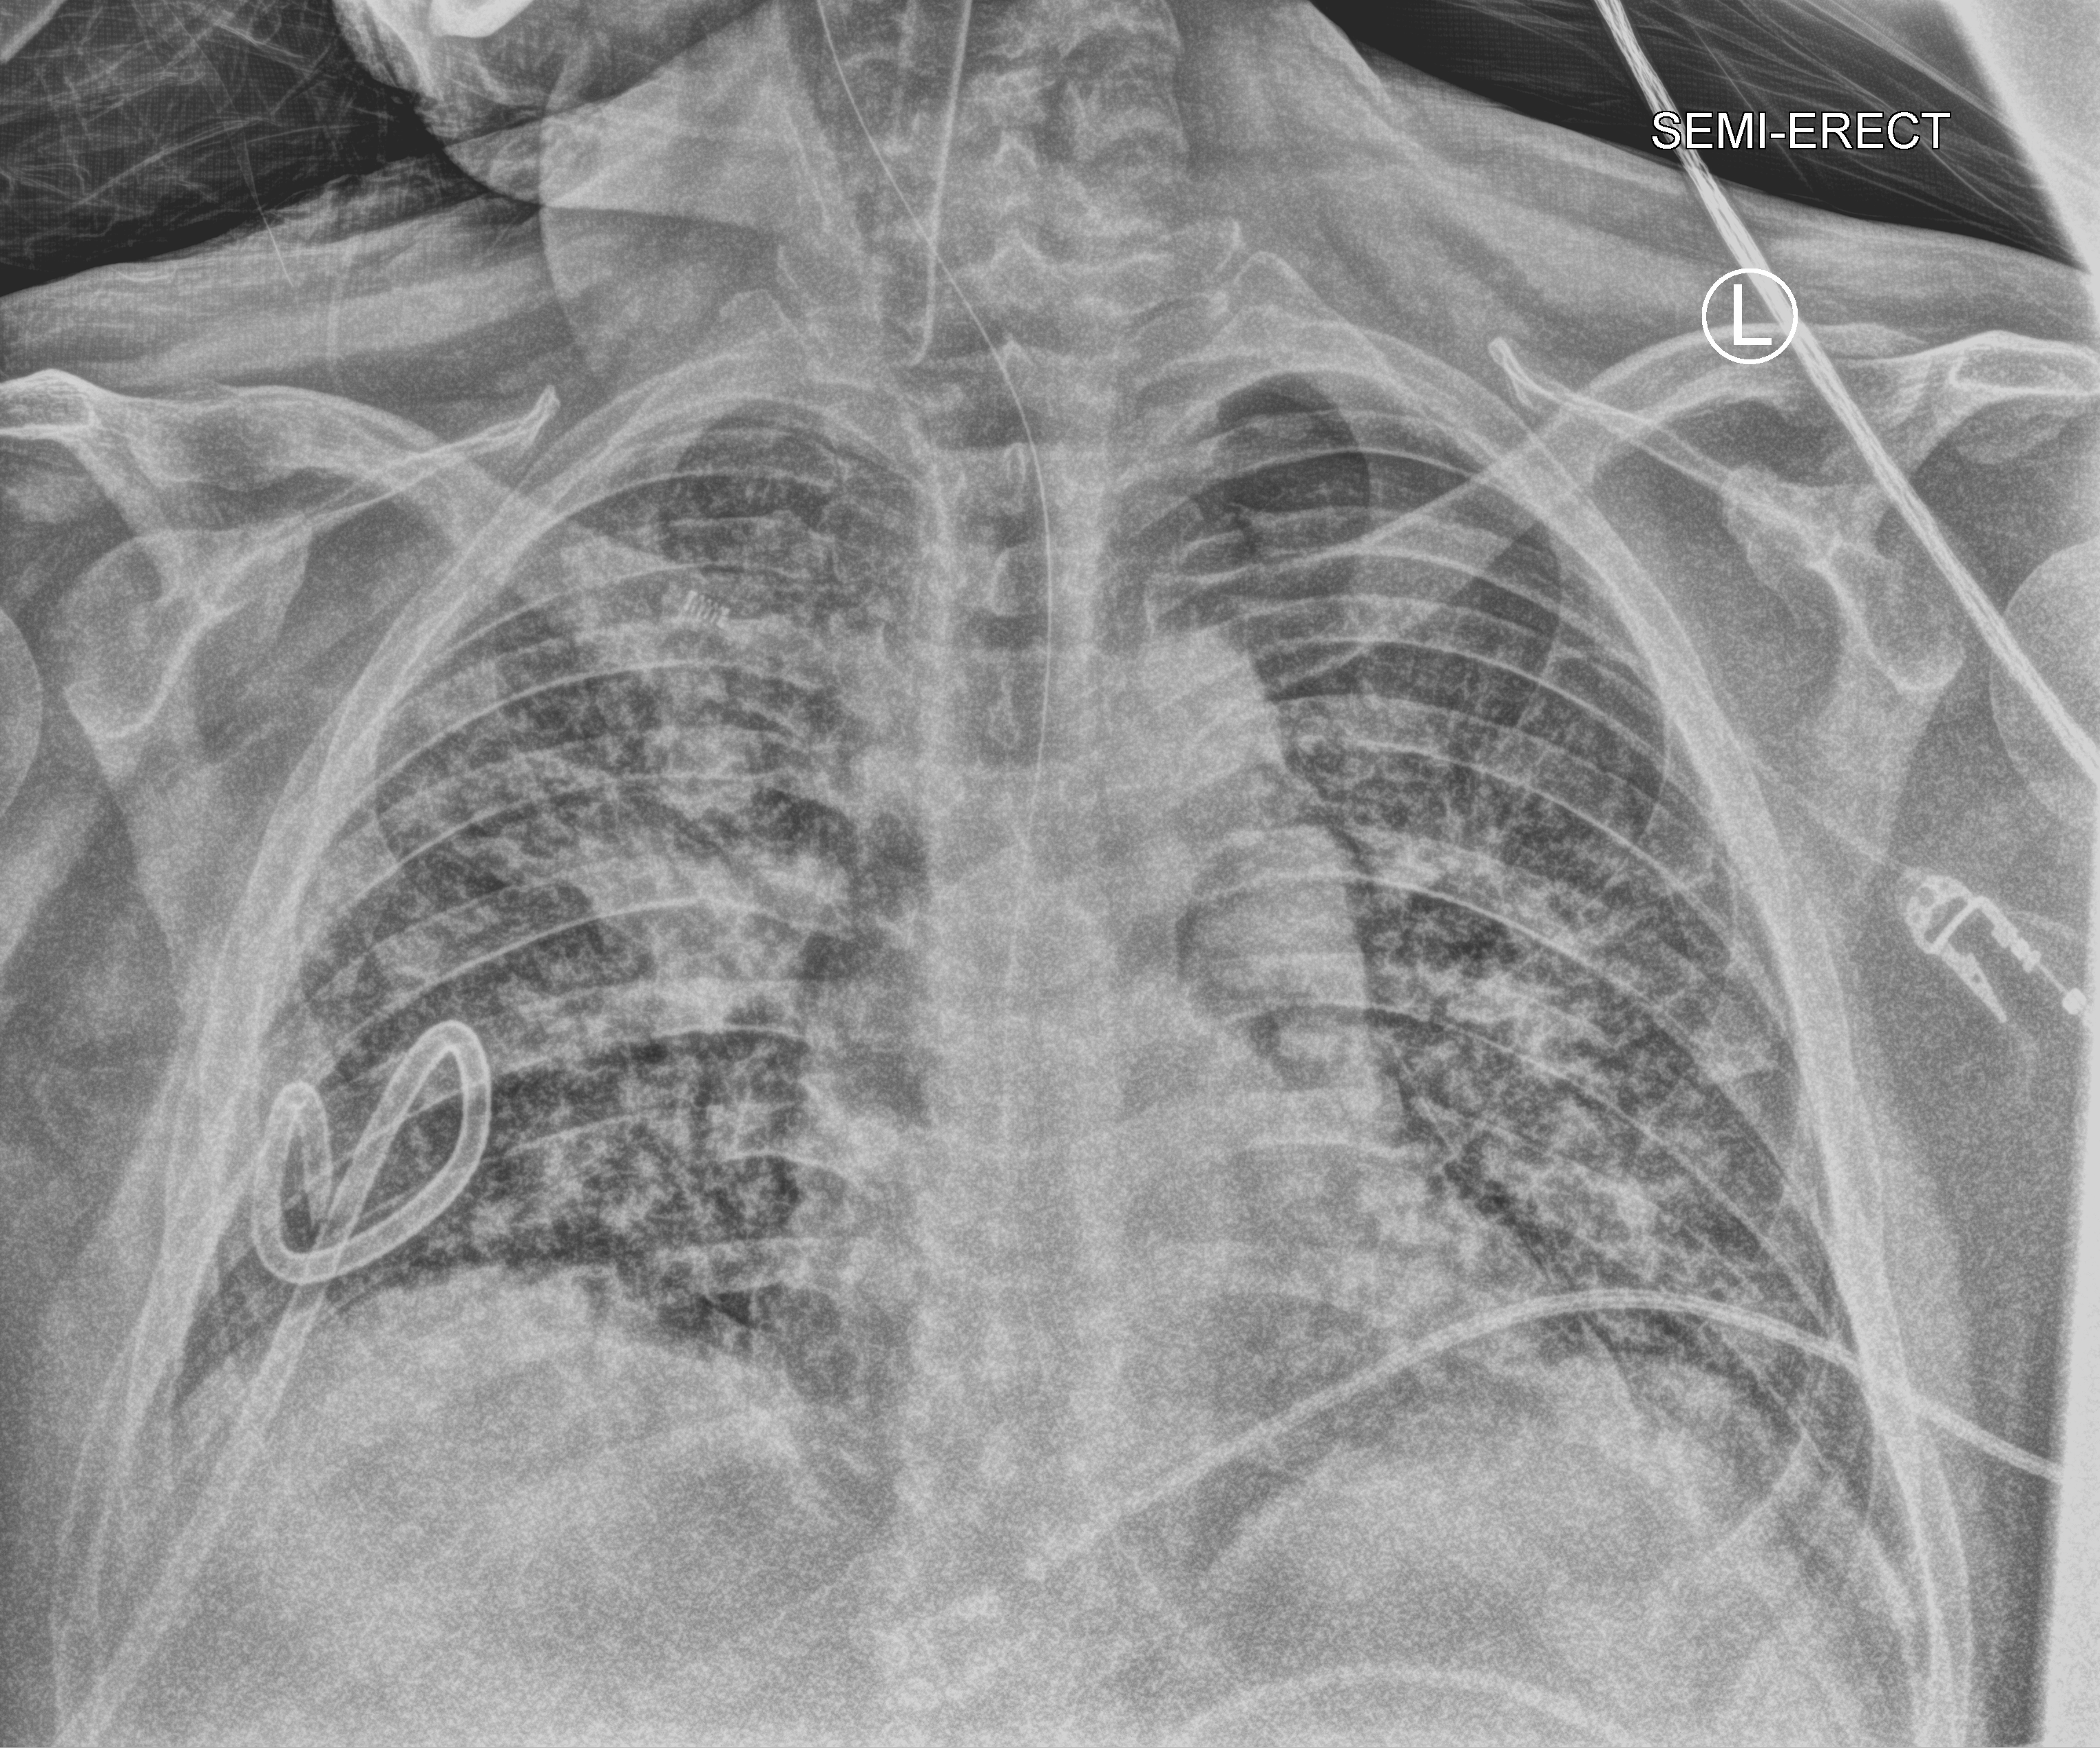
Chest X-ray (portable). Adult patient hospitalised with COVID-19, age 18–59 years.
Hospital-stay facts (about this admission, not read from this image; timing relative to this image not recorded):
- admitted to intensive care during this hospital stay: yes
- mechanically ventilated during this hospital stay: yes